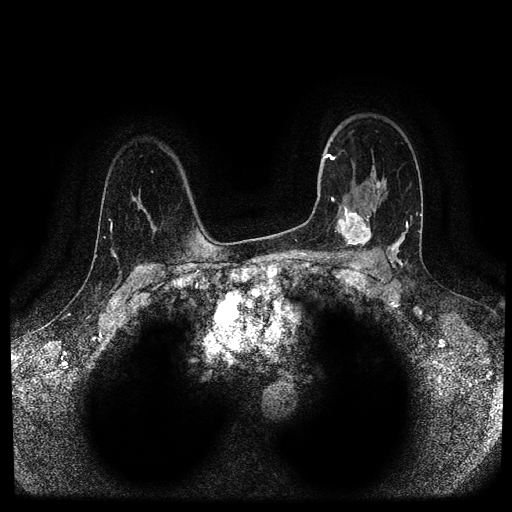
Breast MRI (dynamic contrast-enhanced, multi-phase), one axial slice. Slice 73 of 116 in the series (ordered by position). Dynamic contrast-enhanced series, time point 2 of 5 at this slice position (early post-contrast). 1.5 T. TE 2.6 ms, TR 5.3 ms. 2 mm slice thickness. 512 × 512 image matrix. Female patient, age 44 years.
Structures marked on this image (semi-automatic segmentation, software-assisted and operator-edited):
- breast lesion (labelled 'tumour' in the annotation; benign lesions carry a separate 'benign' label): bounding box [x1, y1, x2, y2] px = [334, 201, 372, 254]